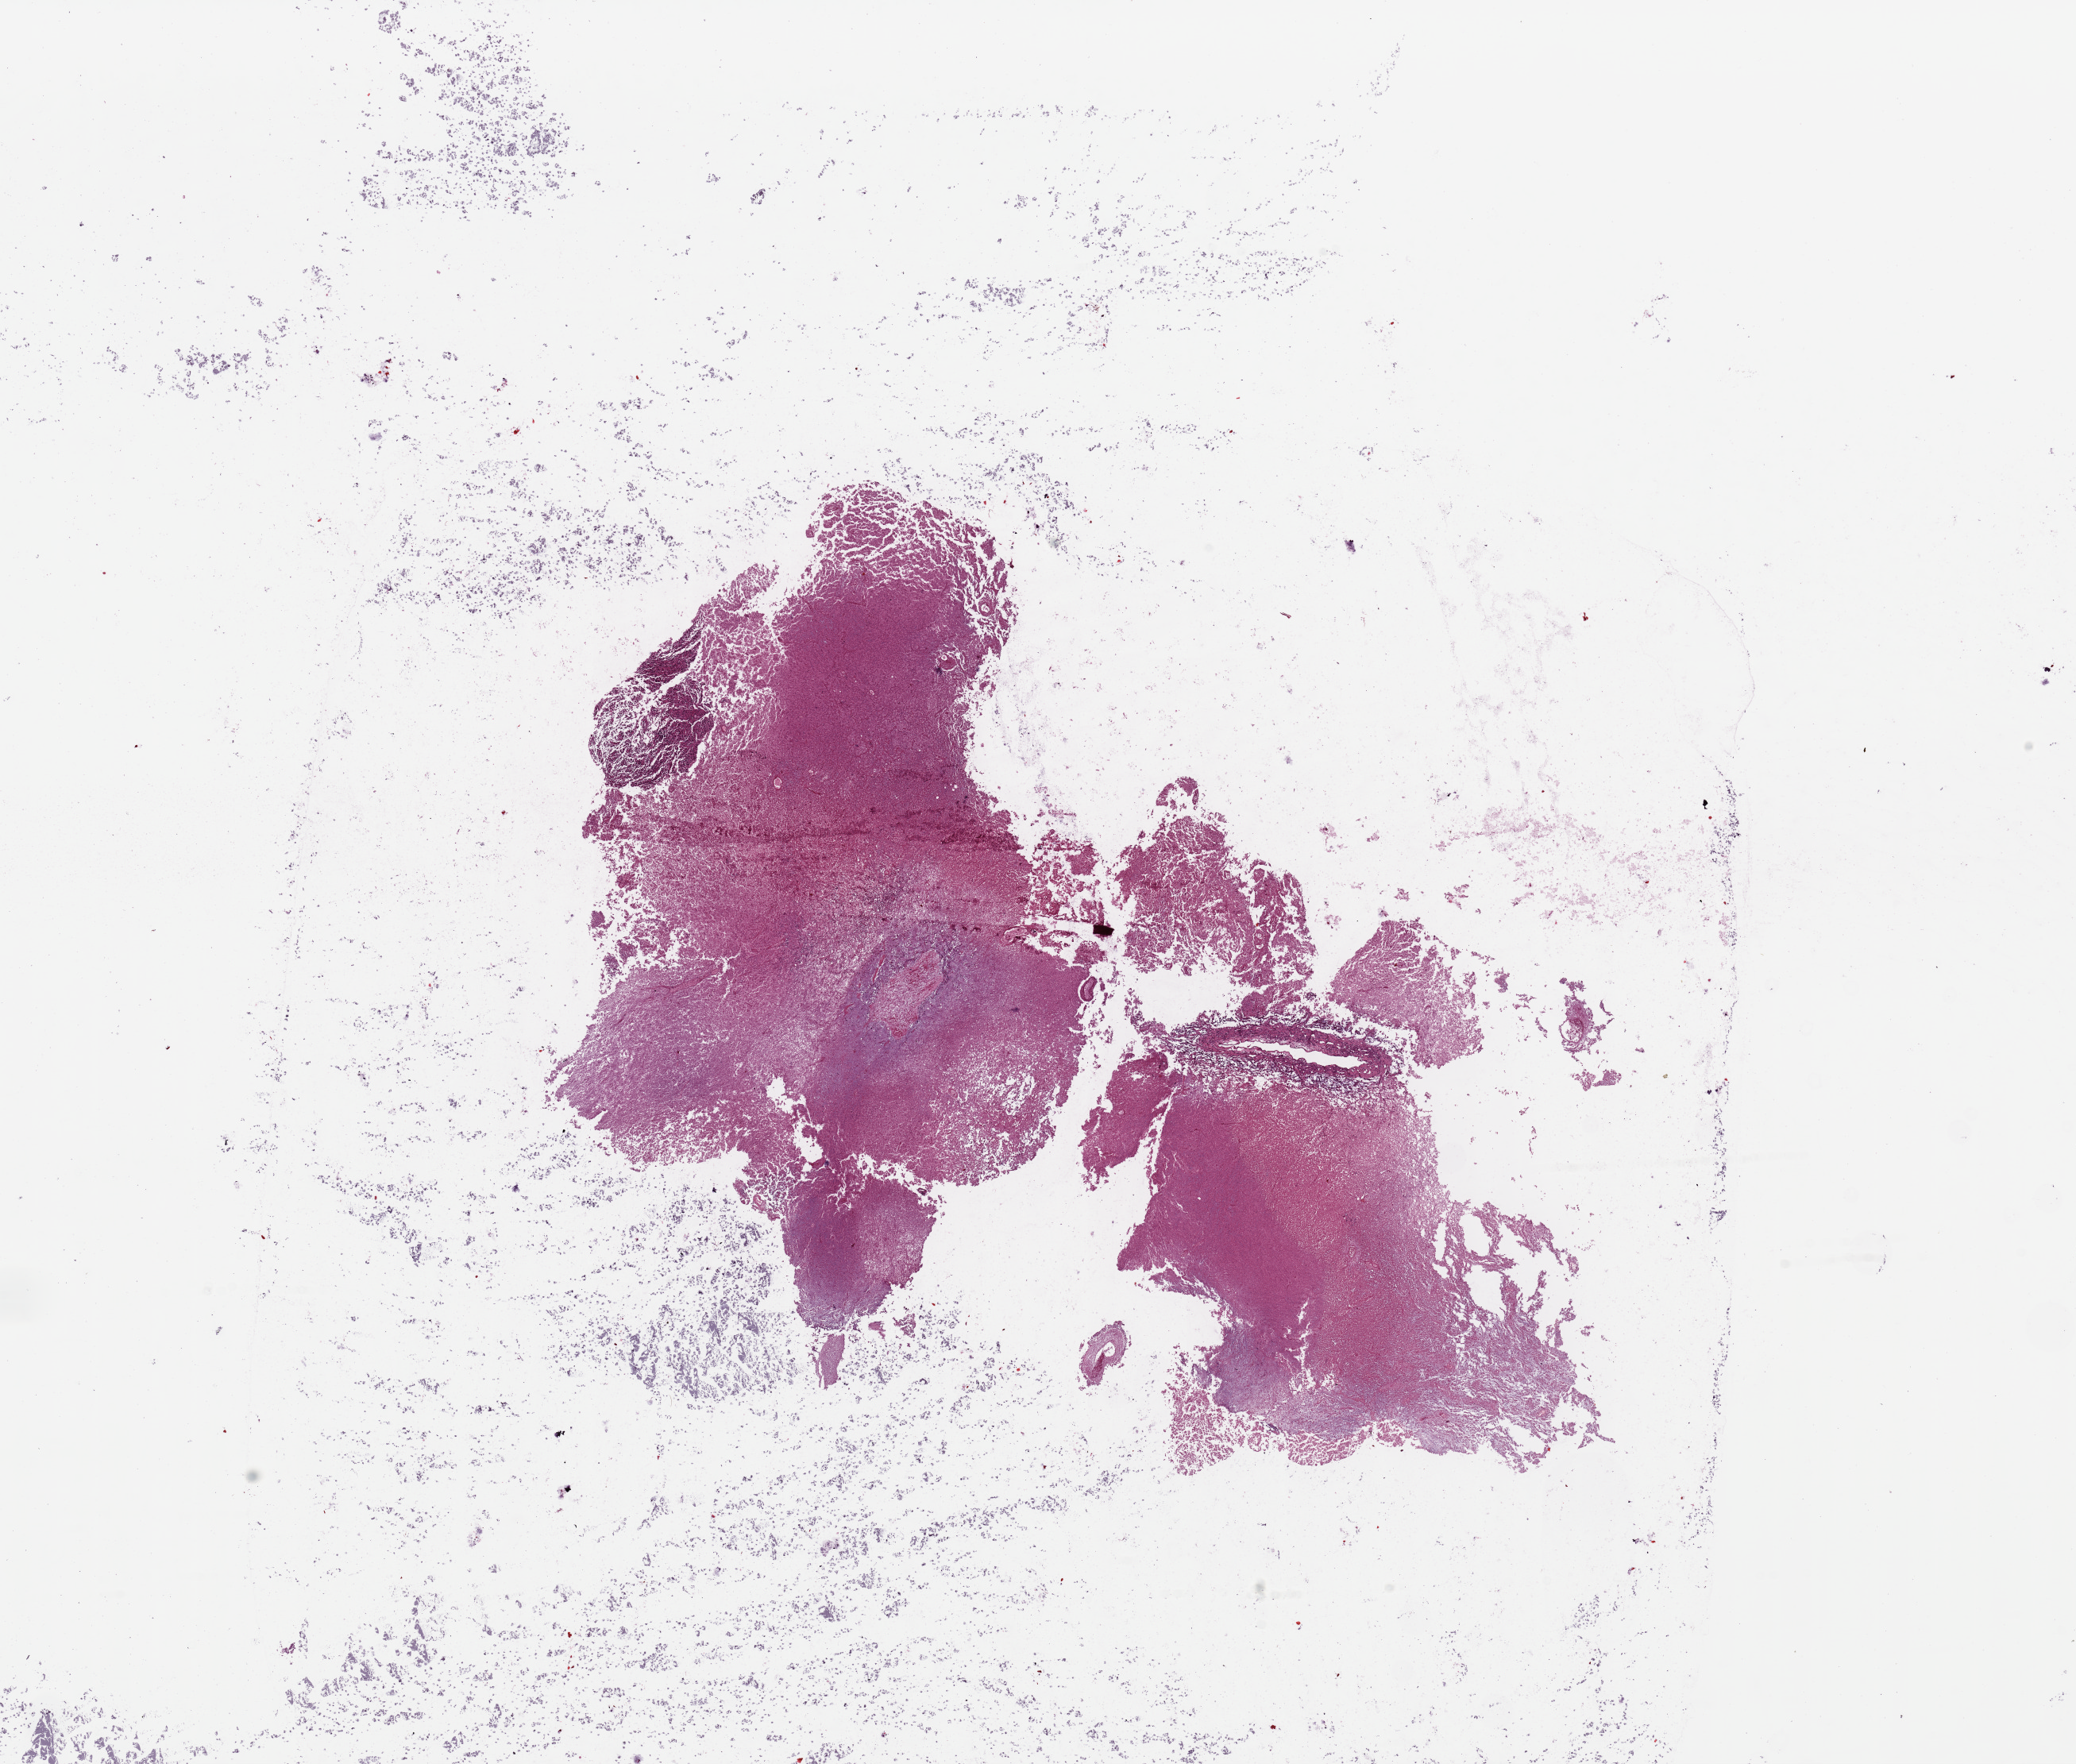
Whole-slide histology image, H&E — low-resolution overview of the scanned area, about 20.7 x 17.6 mm (slide scanned at 20x). Brain, tumour tissue. Patient: female, age 24 years.
Histologic diagnosis: Glioblastoma.